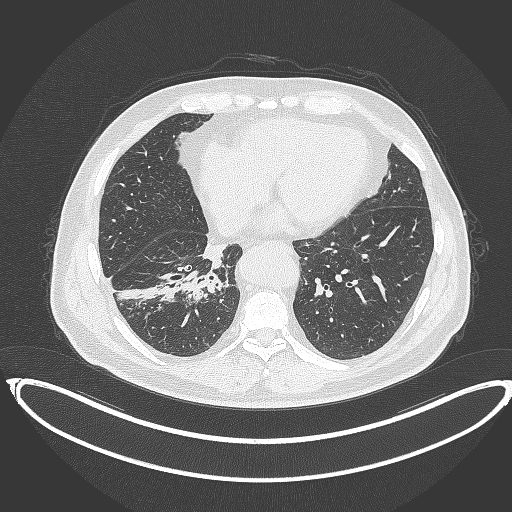
Chest CT, one axial slice. Slice 142 of 387 in the series (ordered by position). Reconstruction kernel B70f. 120 kVp. Lung window (W 1500 / L -600 HU). 512 × 512 image matrix, field of view 448 × 448 mm. Patient: male, 61 years. From the clinical record (not read from this slice): clinical TNM (as recorded): T1b N1 M0.
Outlined on this slice (bounding box drawn by a radiologist):
- lung tumour (recorded histology: squamous cell carcinoma): bounding box [x1, y1, x2, y2] px = [177, 266, 227, 304]